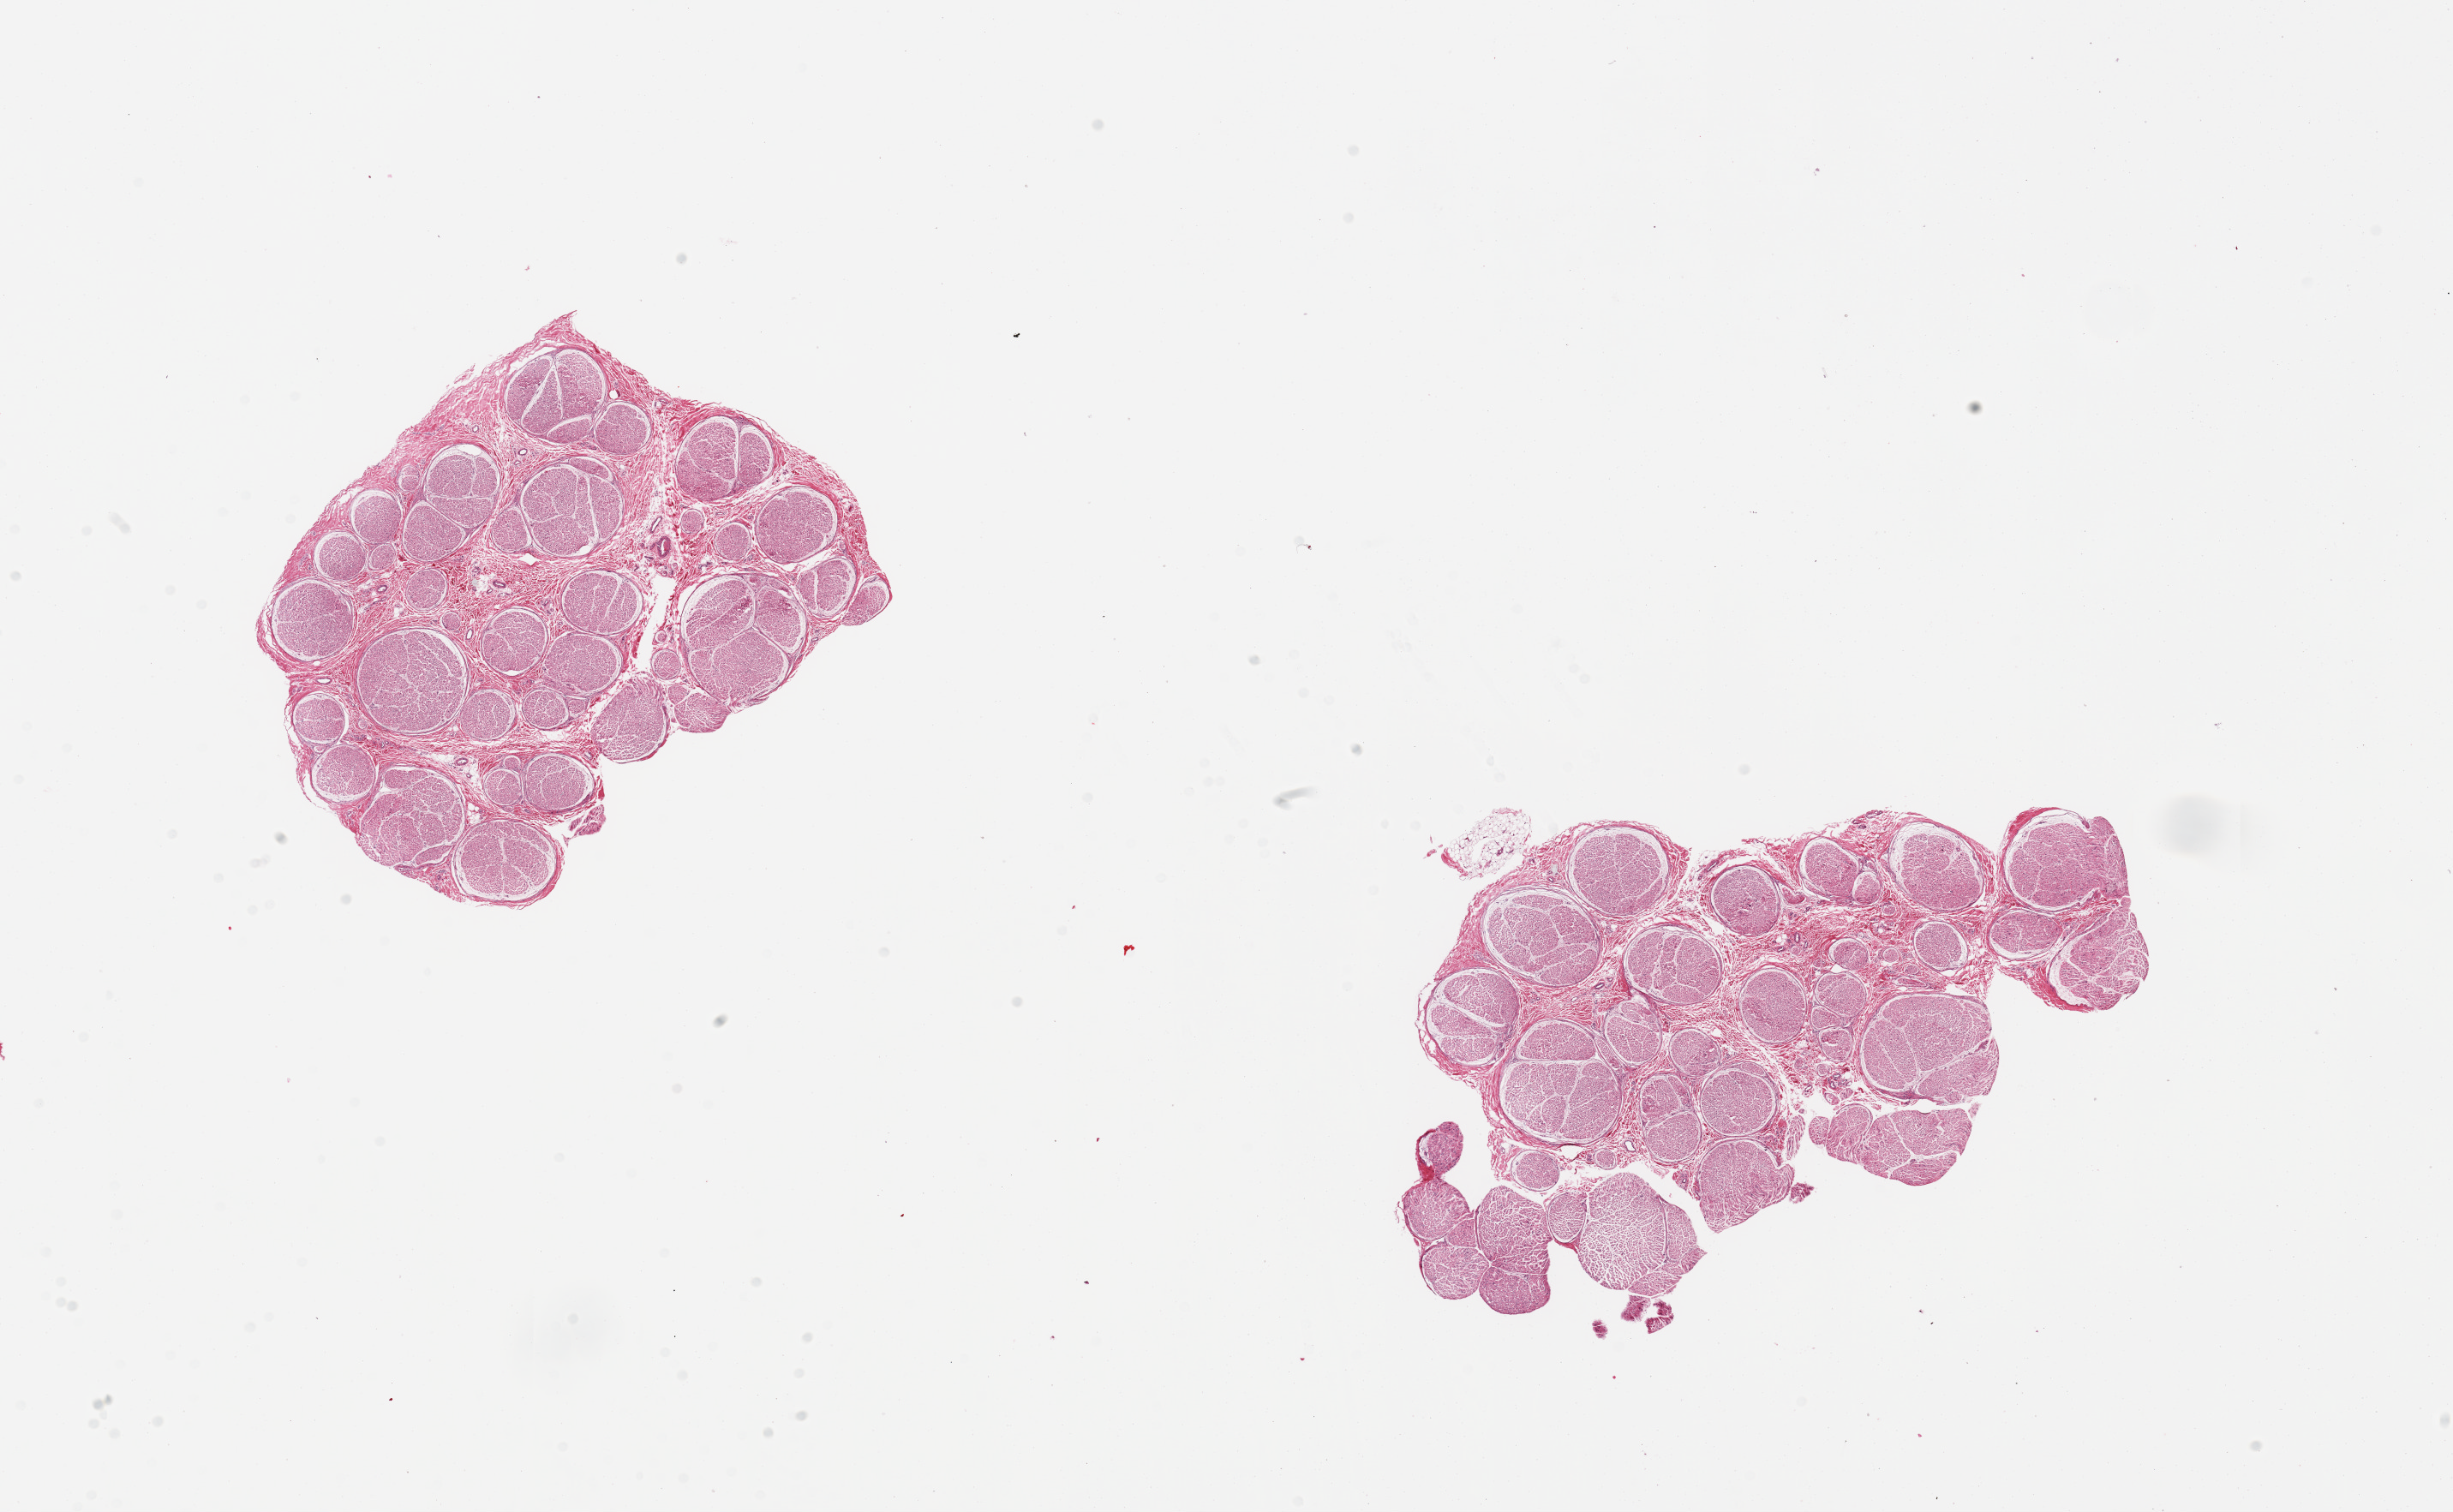
Whole-slide image, H&E stain, brightfield, shown as a low-resolution overview of the whole scanned area (about 22.6 x 14.0 mm, from a 20x scan). PAXgene-fixed paraffin-embedded (PFPE) section. Section of tibial nerve (target tissue). Tissue donor sample. Male donor.
* pathologist's review note for this sample: 2 pieces; well trimmed